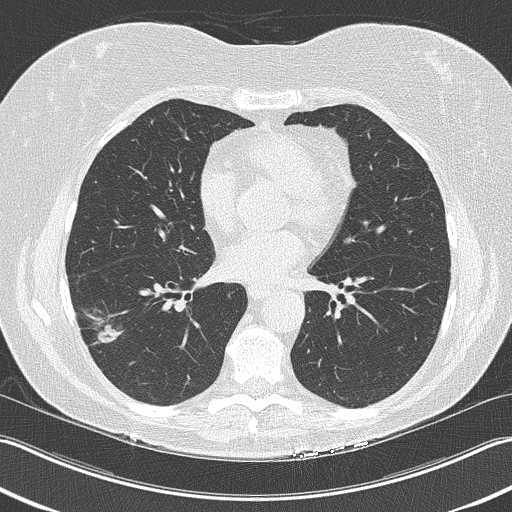
Low-dose screening chest CT, one axial slice. Slice 106 of 210 in the series (ordered by position). 120 kVp. Lung window (W 1500 / L -600 HU). 2 mm slice thickness. 512 × 512 image matrix.
Annotated regions visible in this slice (outlined manually by an expert reader):
- lesion 1 (tumor, lower lobe of right lung): bounding box [x1, y1, x2, y2] px = [96, 324, 124, 344]